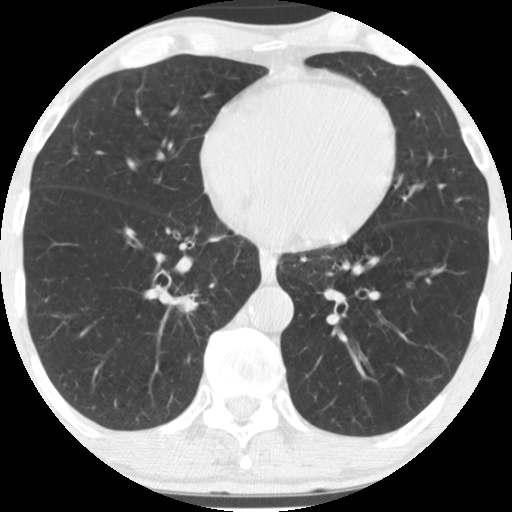
Low-dose screening chest CT, axial slice, first (baseline) screen, lung window (W 1500 / L -600 HU), 2.5 mm slice thickness, slice 111 of 170 in the series. Male, age 67 years at enrolment. Former smoker at enrolment.
Lesion marked by an expert reader, bounding box [x1, y1, x2, y2] px = [151, 267, 212, 333]. The exam's reader record, not a measurement of the box and not confirmed to be the same lesion: non-calcified nodule or mass ≥4 mm, right lower lobe, 16 × 16 mm, spiculated (stellate) margins, soft tissue attenuation. Lung cancer was diagnosed 49 days after this screen: squamous cell carcinoma, NOS, right lower lobe, moderately differentiated (G2), stage IA (AJCC 6th edition), 20 mm at pathology.